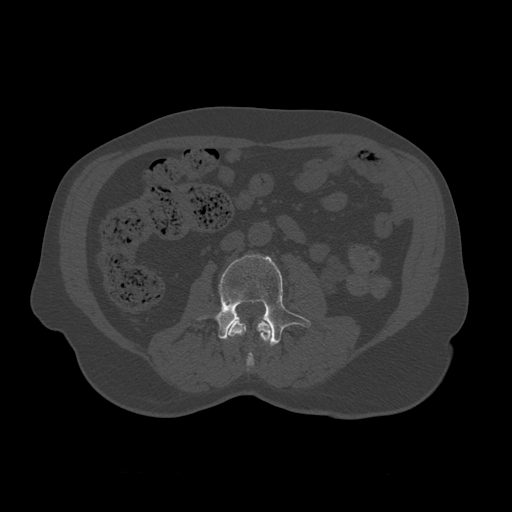
CT including the spine, one axial slice; slice 310 of 450 in the series (ordered by position); reconstruction kernel STANDARD; 120 kVp; bone window (W 1800 / L 400 HU); 1.25 mm slice thickness; 512 × 512 image matrix, field of view 405 × 405 mm. Patient age 75 years. Case-level facts recorded for this patient, not image findings: primary cancer: prostate.
Structures marked on this image (semi-automatic segmentation, software-assisted and operator-edited):
- L2 vertebra: bounding box [x1, y1, x2, y2] px = [228, 318, 272, 372]
- L3 vertebra: [197, 254, 312, 347]